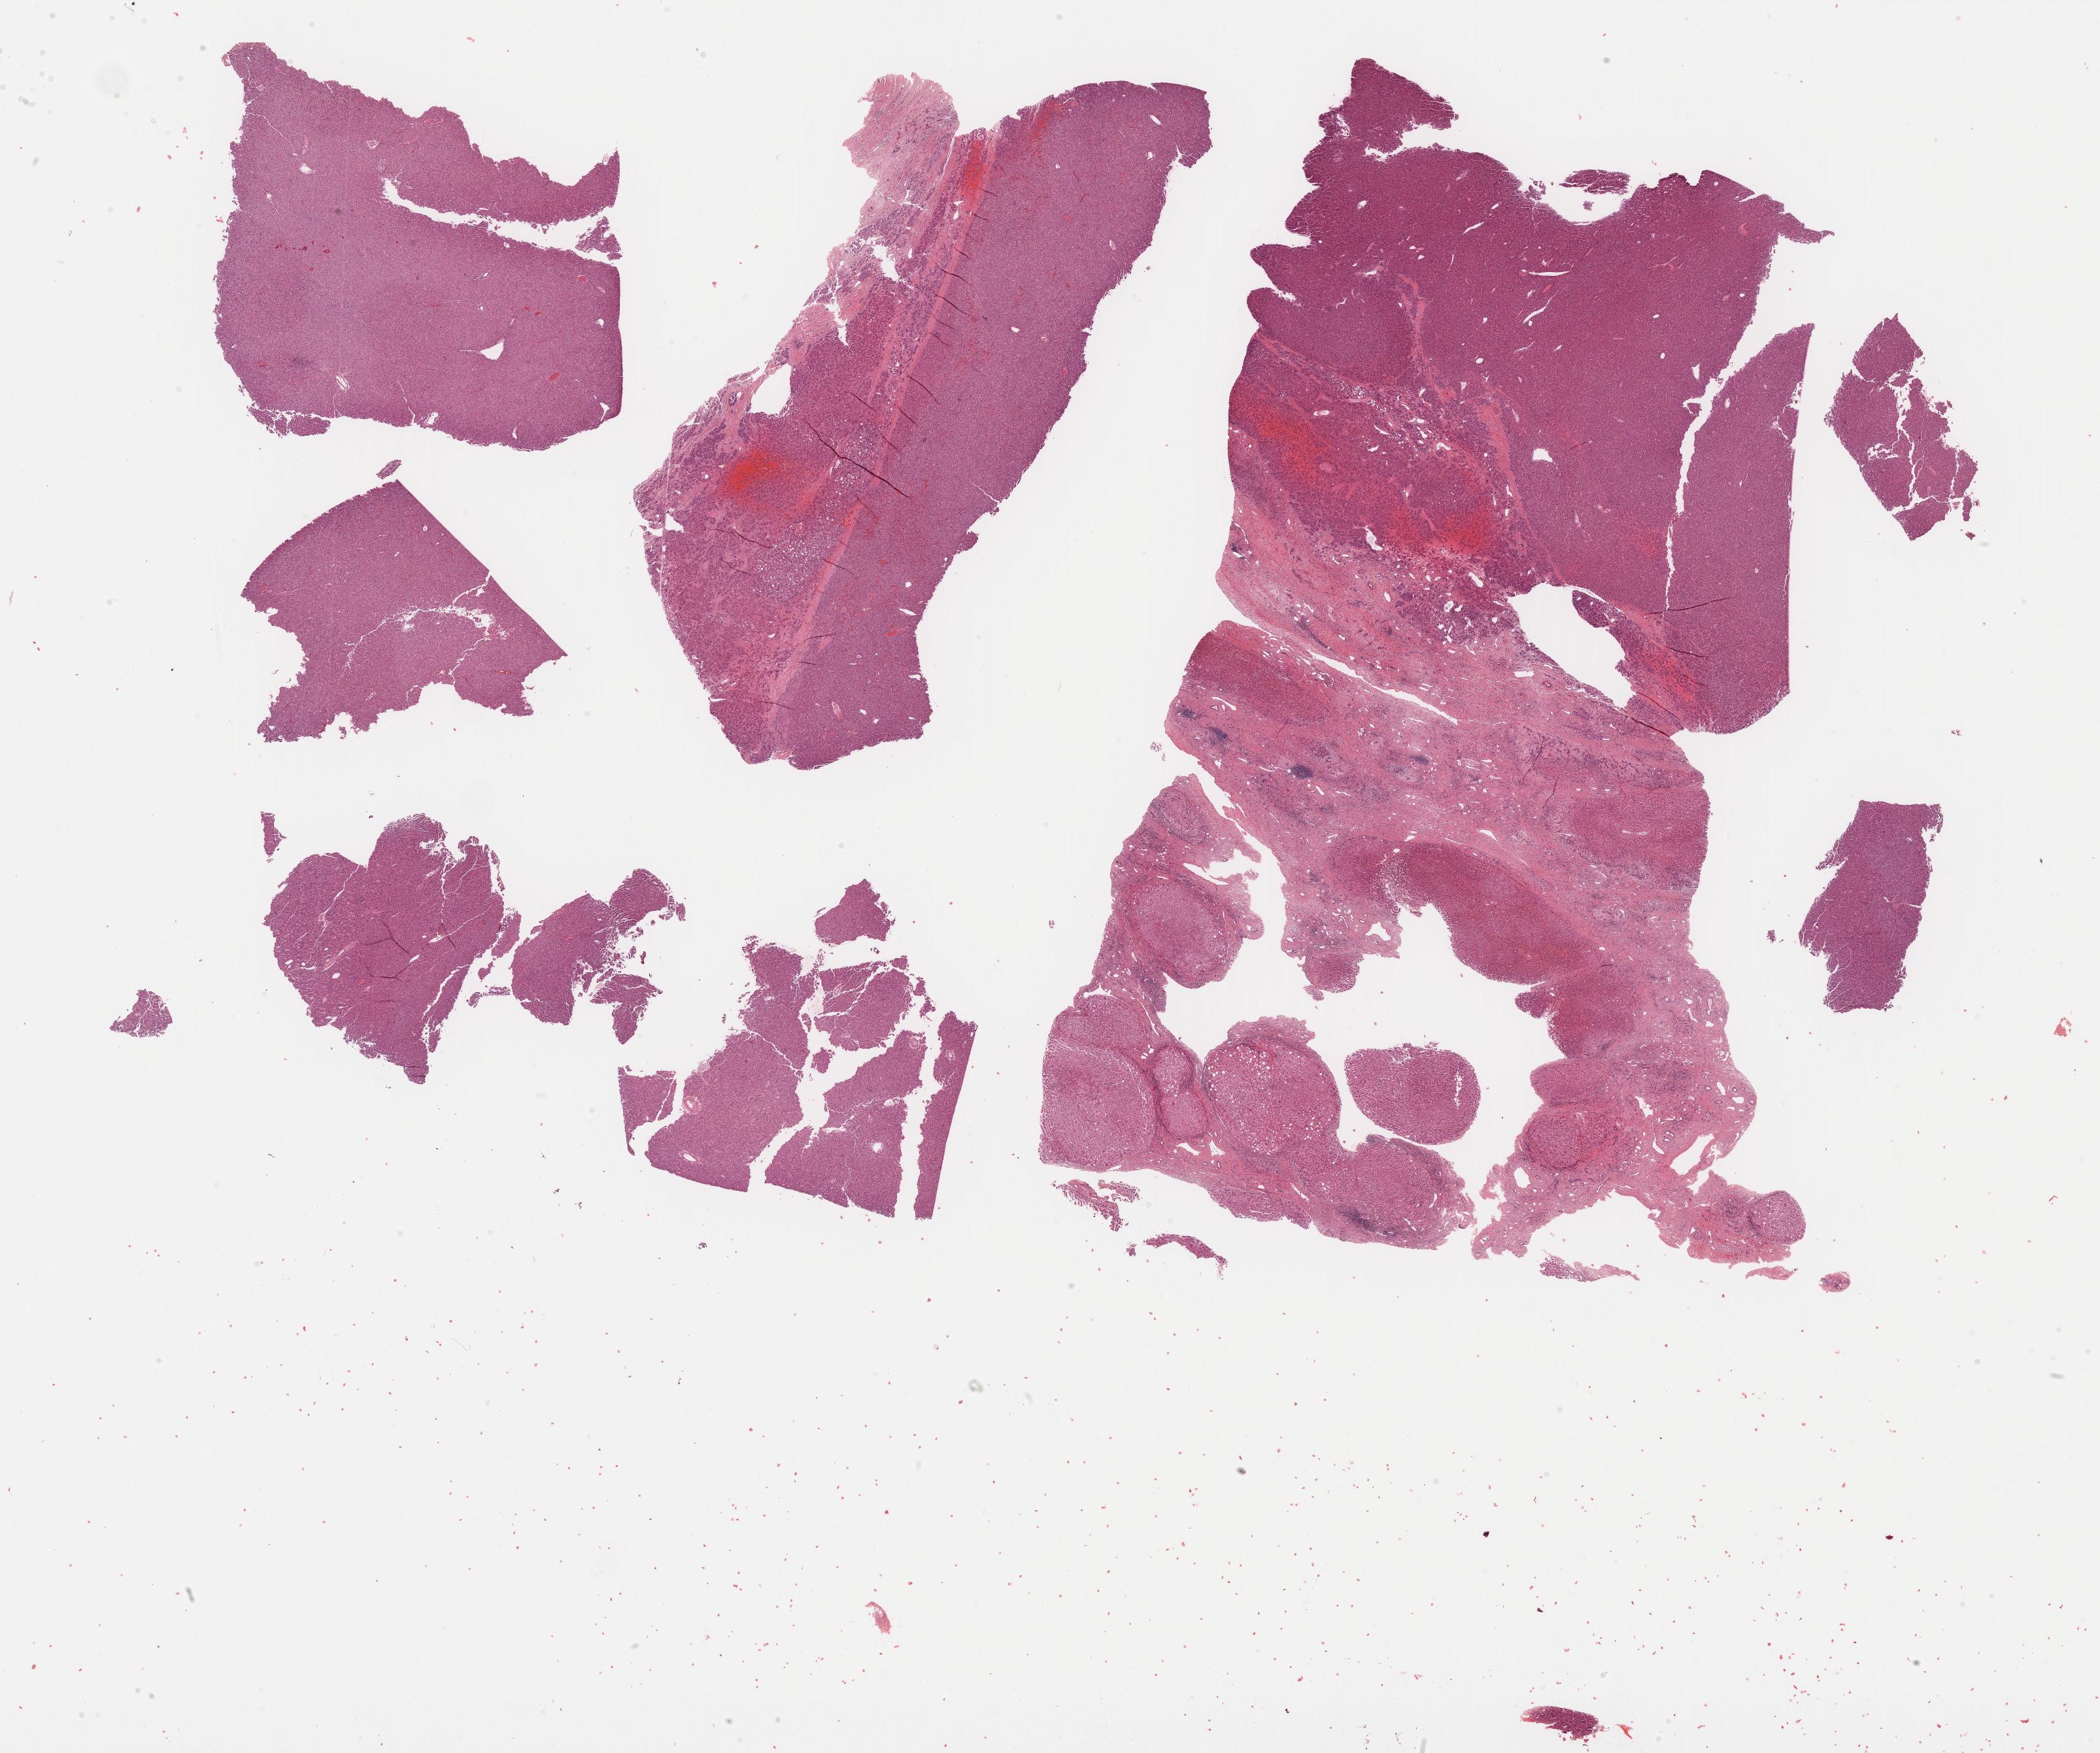
Digitized H&E-stained tissue section (whole slide), whole scanned area (about 26.0 x 21.7 mm) shown as a low-resolution overview, formalin-fixed paraffin-embedded (FFPE) diagnostic section, liver, primary tumour sample. Patient: male, age at initial diagnosis 73 years. Histologic grade: G2 (moderately differentiated).
AJCC pathologic stage: I (6th edition). TNM: T1 N0 M0. Histologic diagnosis: Hepatocellular carcinoma, NOS.